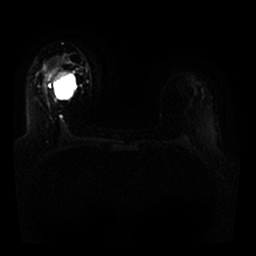
Breast MRI, one axial slice. Slice 16 of 25 in the series (ordered by position). Diffusion-weighted series; image 2 of 4 stored at this slice position (different b-values; order by instance number). 1.5 T. 256 × 256 image matrix, field of view 330 × 330 mm. Female patient.
Structures marked on this image (manually delineated by an expert):
- tumour on diffusion-weighted imaging: bounding box (x1, y1, x2, y2) in pixels: (54, 71, 70, 81)